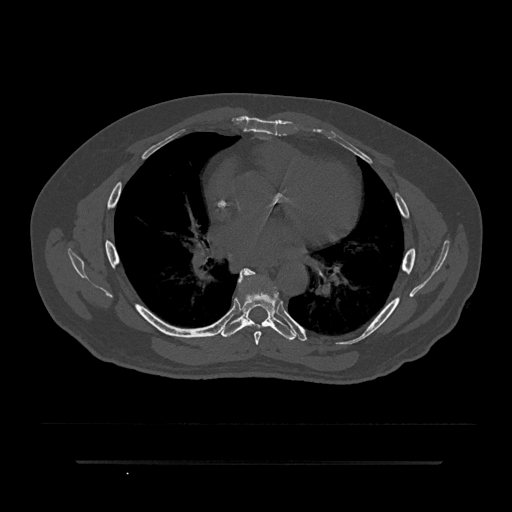
CT including the spine, one axial slice. Slice 498 of 797 in the series (ordered by position). Reconstruction kernel Br40s/3. Bone window (W 1800 / L 400 HU). 0.5 mm slice thickness. 512 × 512 image matrix, field of view 464 × 464 mm. Patient: male, 59 years. Case-level facts recorded for this patient, not image findings: primary cancer: bile ducts; vertebrae with lytic lesions (as recorded): T10.
Annotated regions visible in this slice (semi-automatic segmentation, software-assisted and operator-edited):
- T6 vertebra: bounding box [x1, y1, x2, y2] px = [238, 270, 261, 345]
- T7 vertebra: [221, 268, 296, 341]